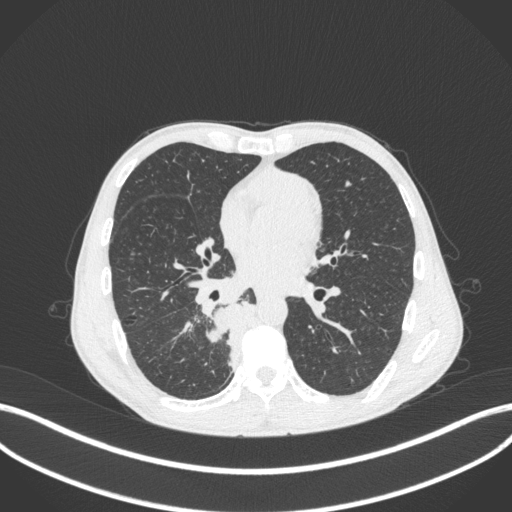
Chest CT, one axial slice. Position 180 of 371 along the scan axis. 120 kVp. Lung window (W 1500 / L -600 HU). 1 mm slice thickness. 512 × 512 image matrix, field of view 400 × 400 mm. Male patient, age 58 years. Case-level facts recorded for this patient, not image findings: clinical TNM (as recorded): T3 N1 M1.
Annotated regions visible in this slice (rectangle marked by the reading radiologist):
- lung tumour (recorded histology: squamous cell carcinoma): bounding box <207,299,265,373> (left, top, right, bottom; pixels)